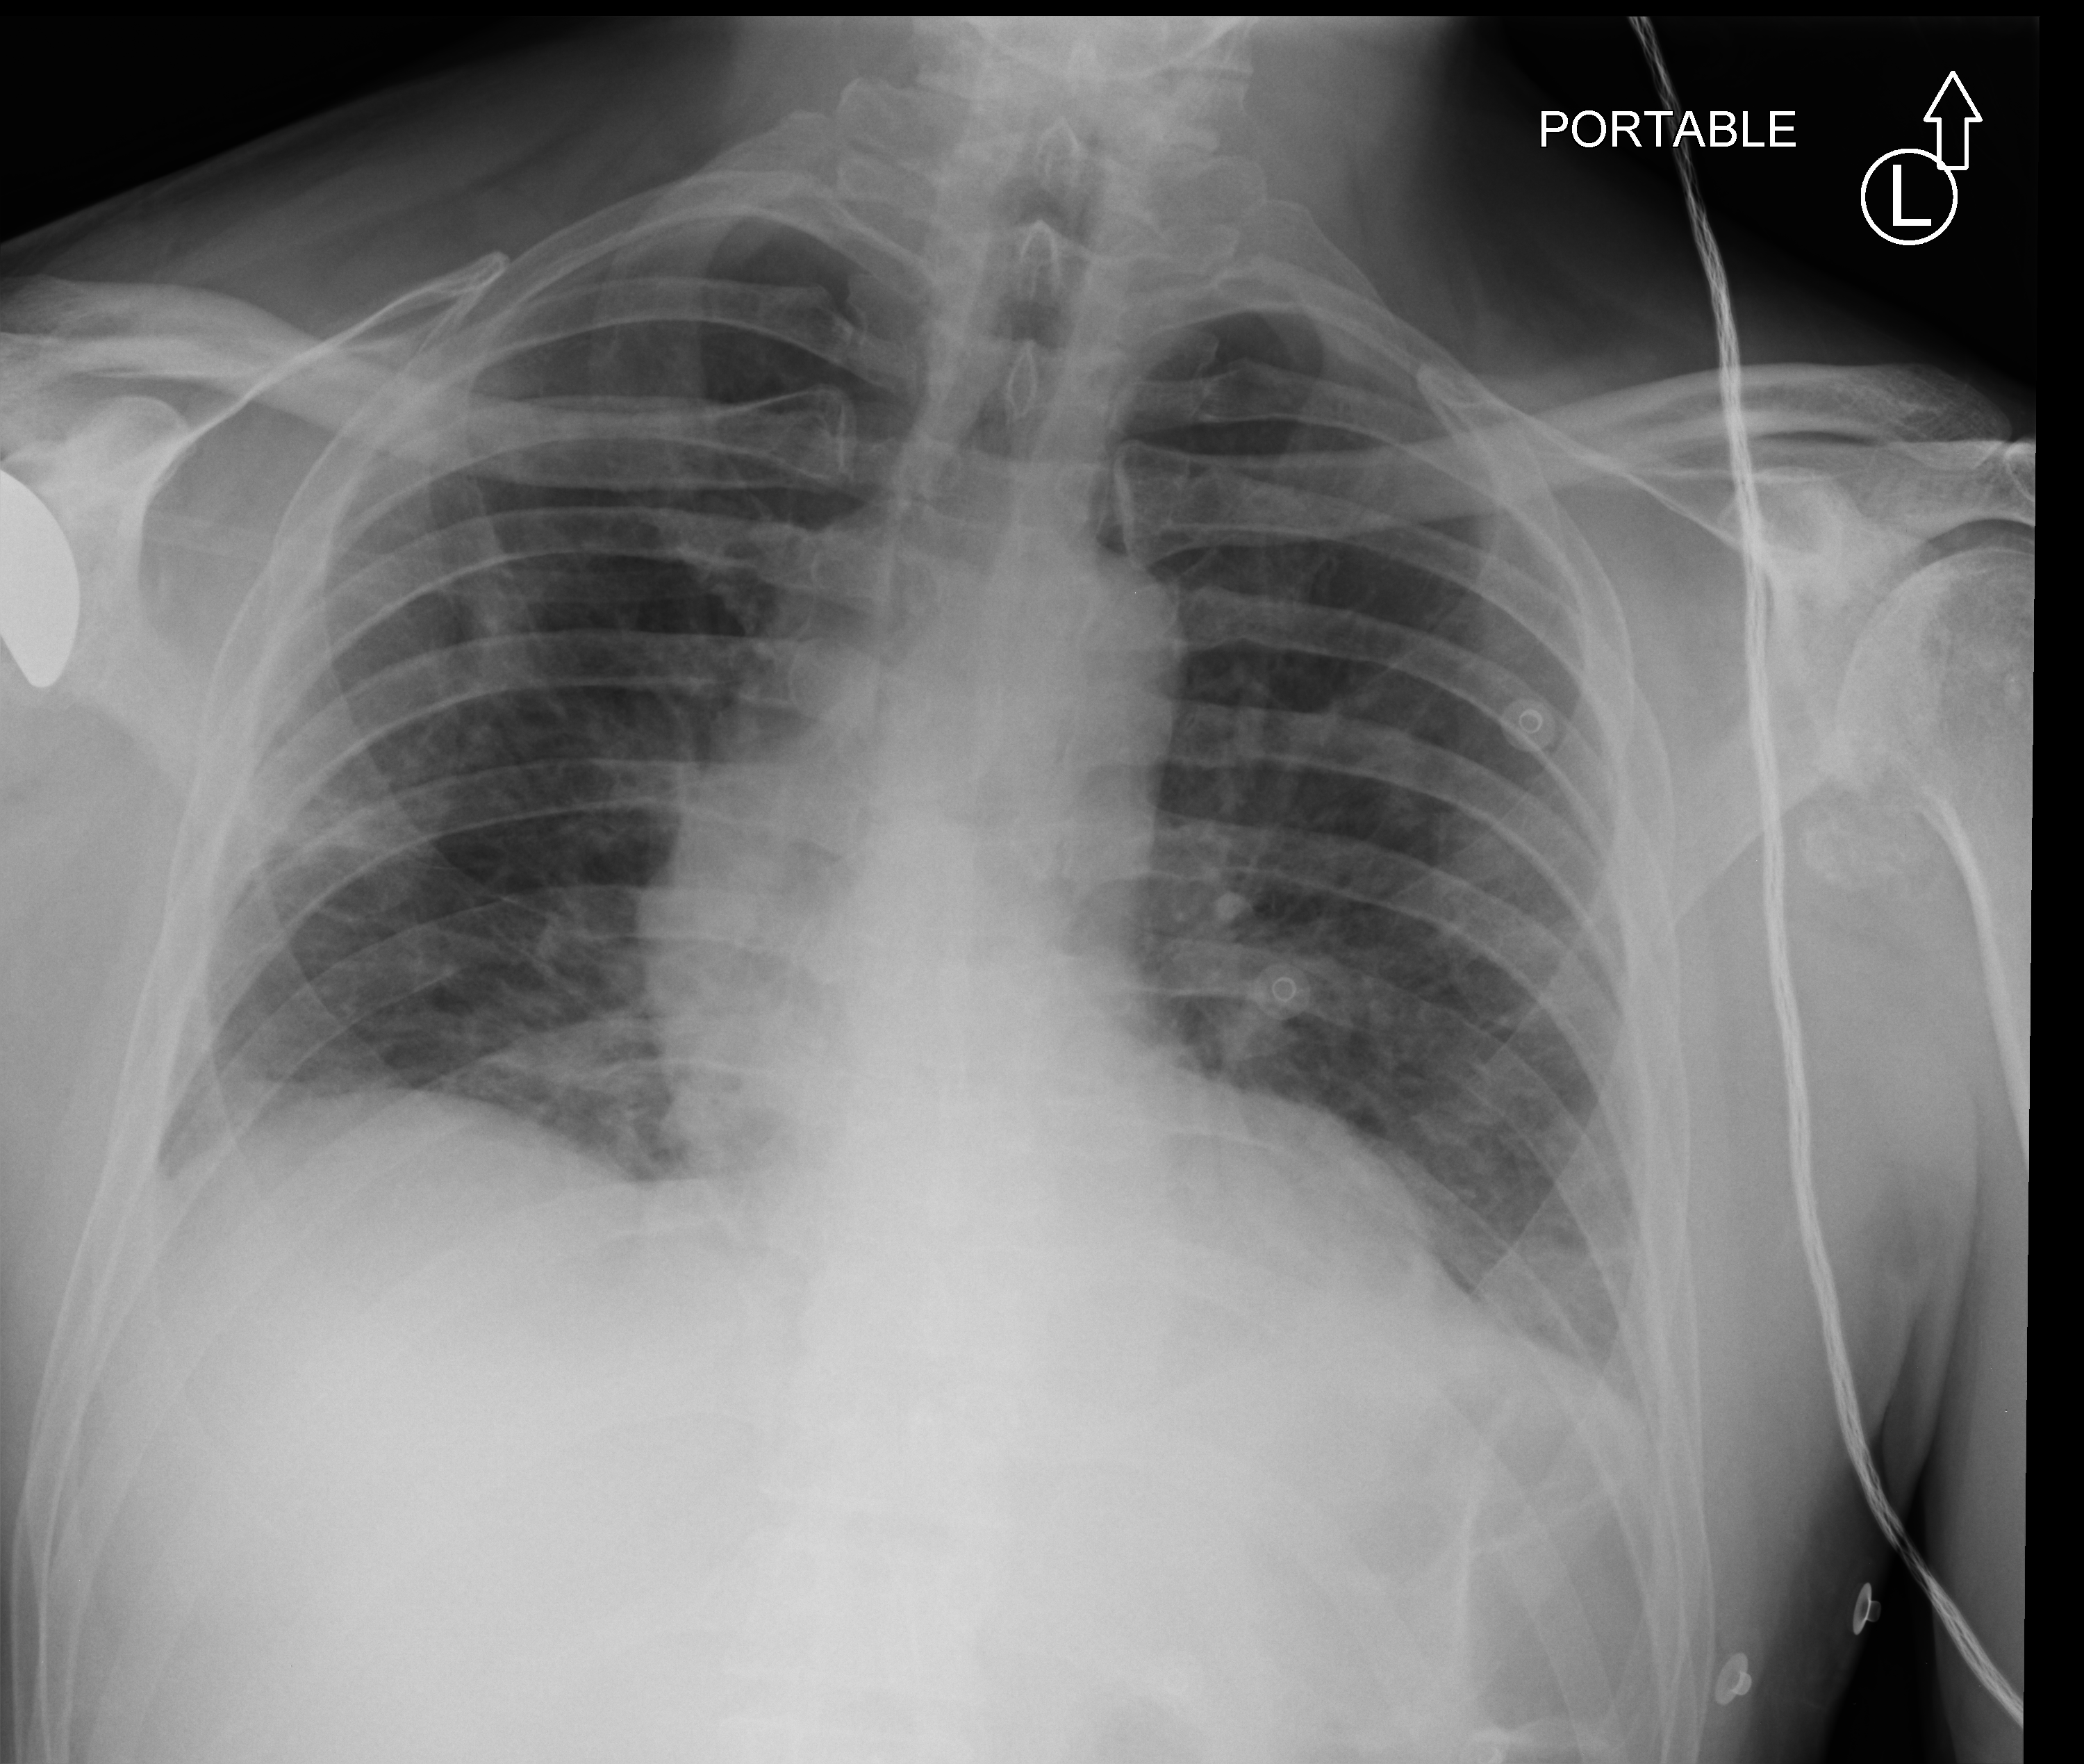
Bedside chest radiograph (computed radiography), anteroposterior (AP) projection. Patient hospitalised with COVID-19; male, aged 60–74 years.
From the hospital-stay record, not from the radiograph (when in the stay this image was taken is not recorded): smoking status (admission record): never; admitted to intensive care during this hospital stay: no.